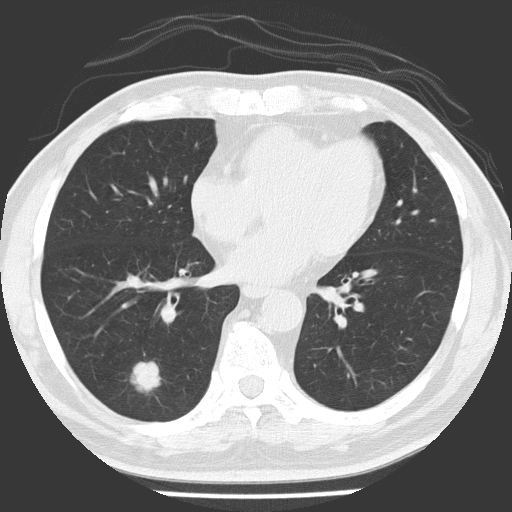
Low-dose screening chest CT, one axial slice. Position 67 of 154 along the scan axis. Reconstruction kernel FC51. 120 kVp. Lung window (W 1500 / L -600 HU). 2 mm slice thickness. 512 × 512 image matrix, field of view 311 × 311 mm.
Annotated regions visible in this slice (outlined manually by an expert reader):
- lesion 1 (tumor, lower lobe of right lung): box from (x=131, y=362) to (x=161, y=391) px